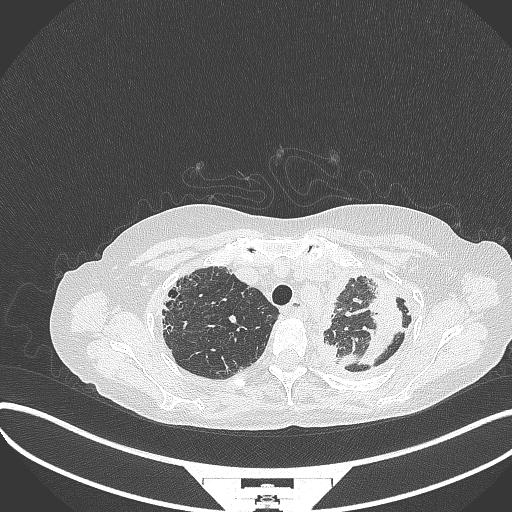
Chest CT, one axial slice; slice 279 of 373 in the series (ordered by position); reconstruction kernel B70f; 120 kVp; lung window (W 1500 / L -600 HU); 1 mm slice thickness; 512 × 512 image matrix, field of view 400 × 400 mm. Patient: female, 56 years. Case-level facts recorded for this patient, not image findings: clinical TNM (as recorded): T1 N0 M0.
Structures marked on this image (rectangle marked by the reading radiologist):
- lung tumour (recorded histology: adenocarcinoma): box from (x=358, y=277) to (x=407, y=370) px